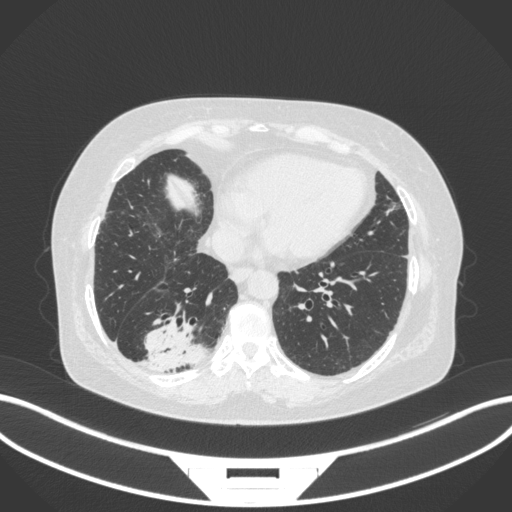
Chest CT, one axial slice; slice 70 of 303 in the series (ordered by position); reconstruction kernel B31f; 120 kVp; lung window (W 1500 / L -600 HU); 1 mm slice thickness; 512 × 512 image matrix, field of view 400 × 400 mm. Patient: female, 65 years. Case-level facts recorded for this patient, not image findings: clinical TNM (as recorded): T2b N1 M0; histopathological grade: G1.
Outlined on this slice (bounding box drawn by a radiologist):
- lung tumour (recorded histology: adenocarcinoma): bounding box (x1, y1, x2, y2) in pixels: (134, 319, 212, 372)